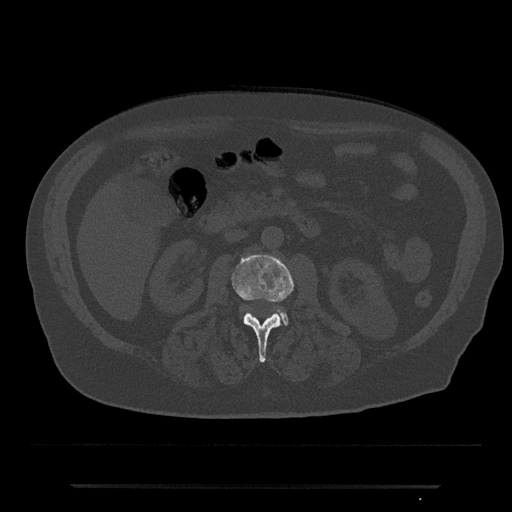
CT including the spine, one axial slice; position 454 of 797 along the scan axis; reconstruction kernel Br40s/3; 120 kVp; bone window (W 1800 / L 400 HU); 512 × 512 image matrix, field of view 434 × 434 mm. Male patient, age 80 years. From the clinical record (not read from this slice): primary cancer: prostate; vertebrae with lytic lesions (as recorded): L1, T11.
Annotated regions visible in this slice (semi-automatic segmentation, software-assisted and operator-edited):
- L2 vertebra: bounding box [x1, y1, x2, y2] px = [232, 255, 294, 363]
- L3 vertebra: [277, 310, 289, 325]